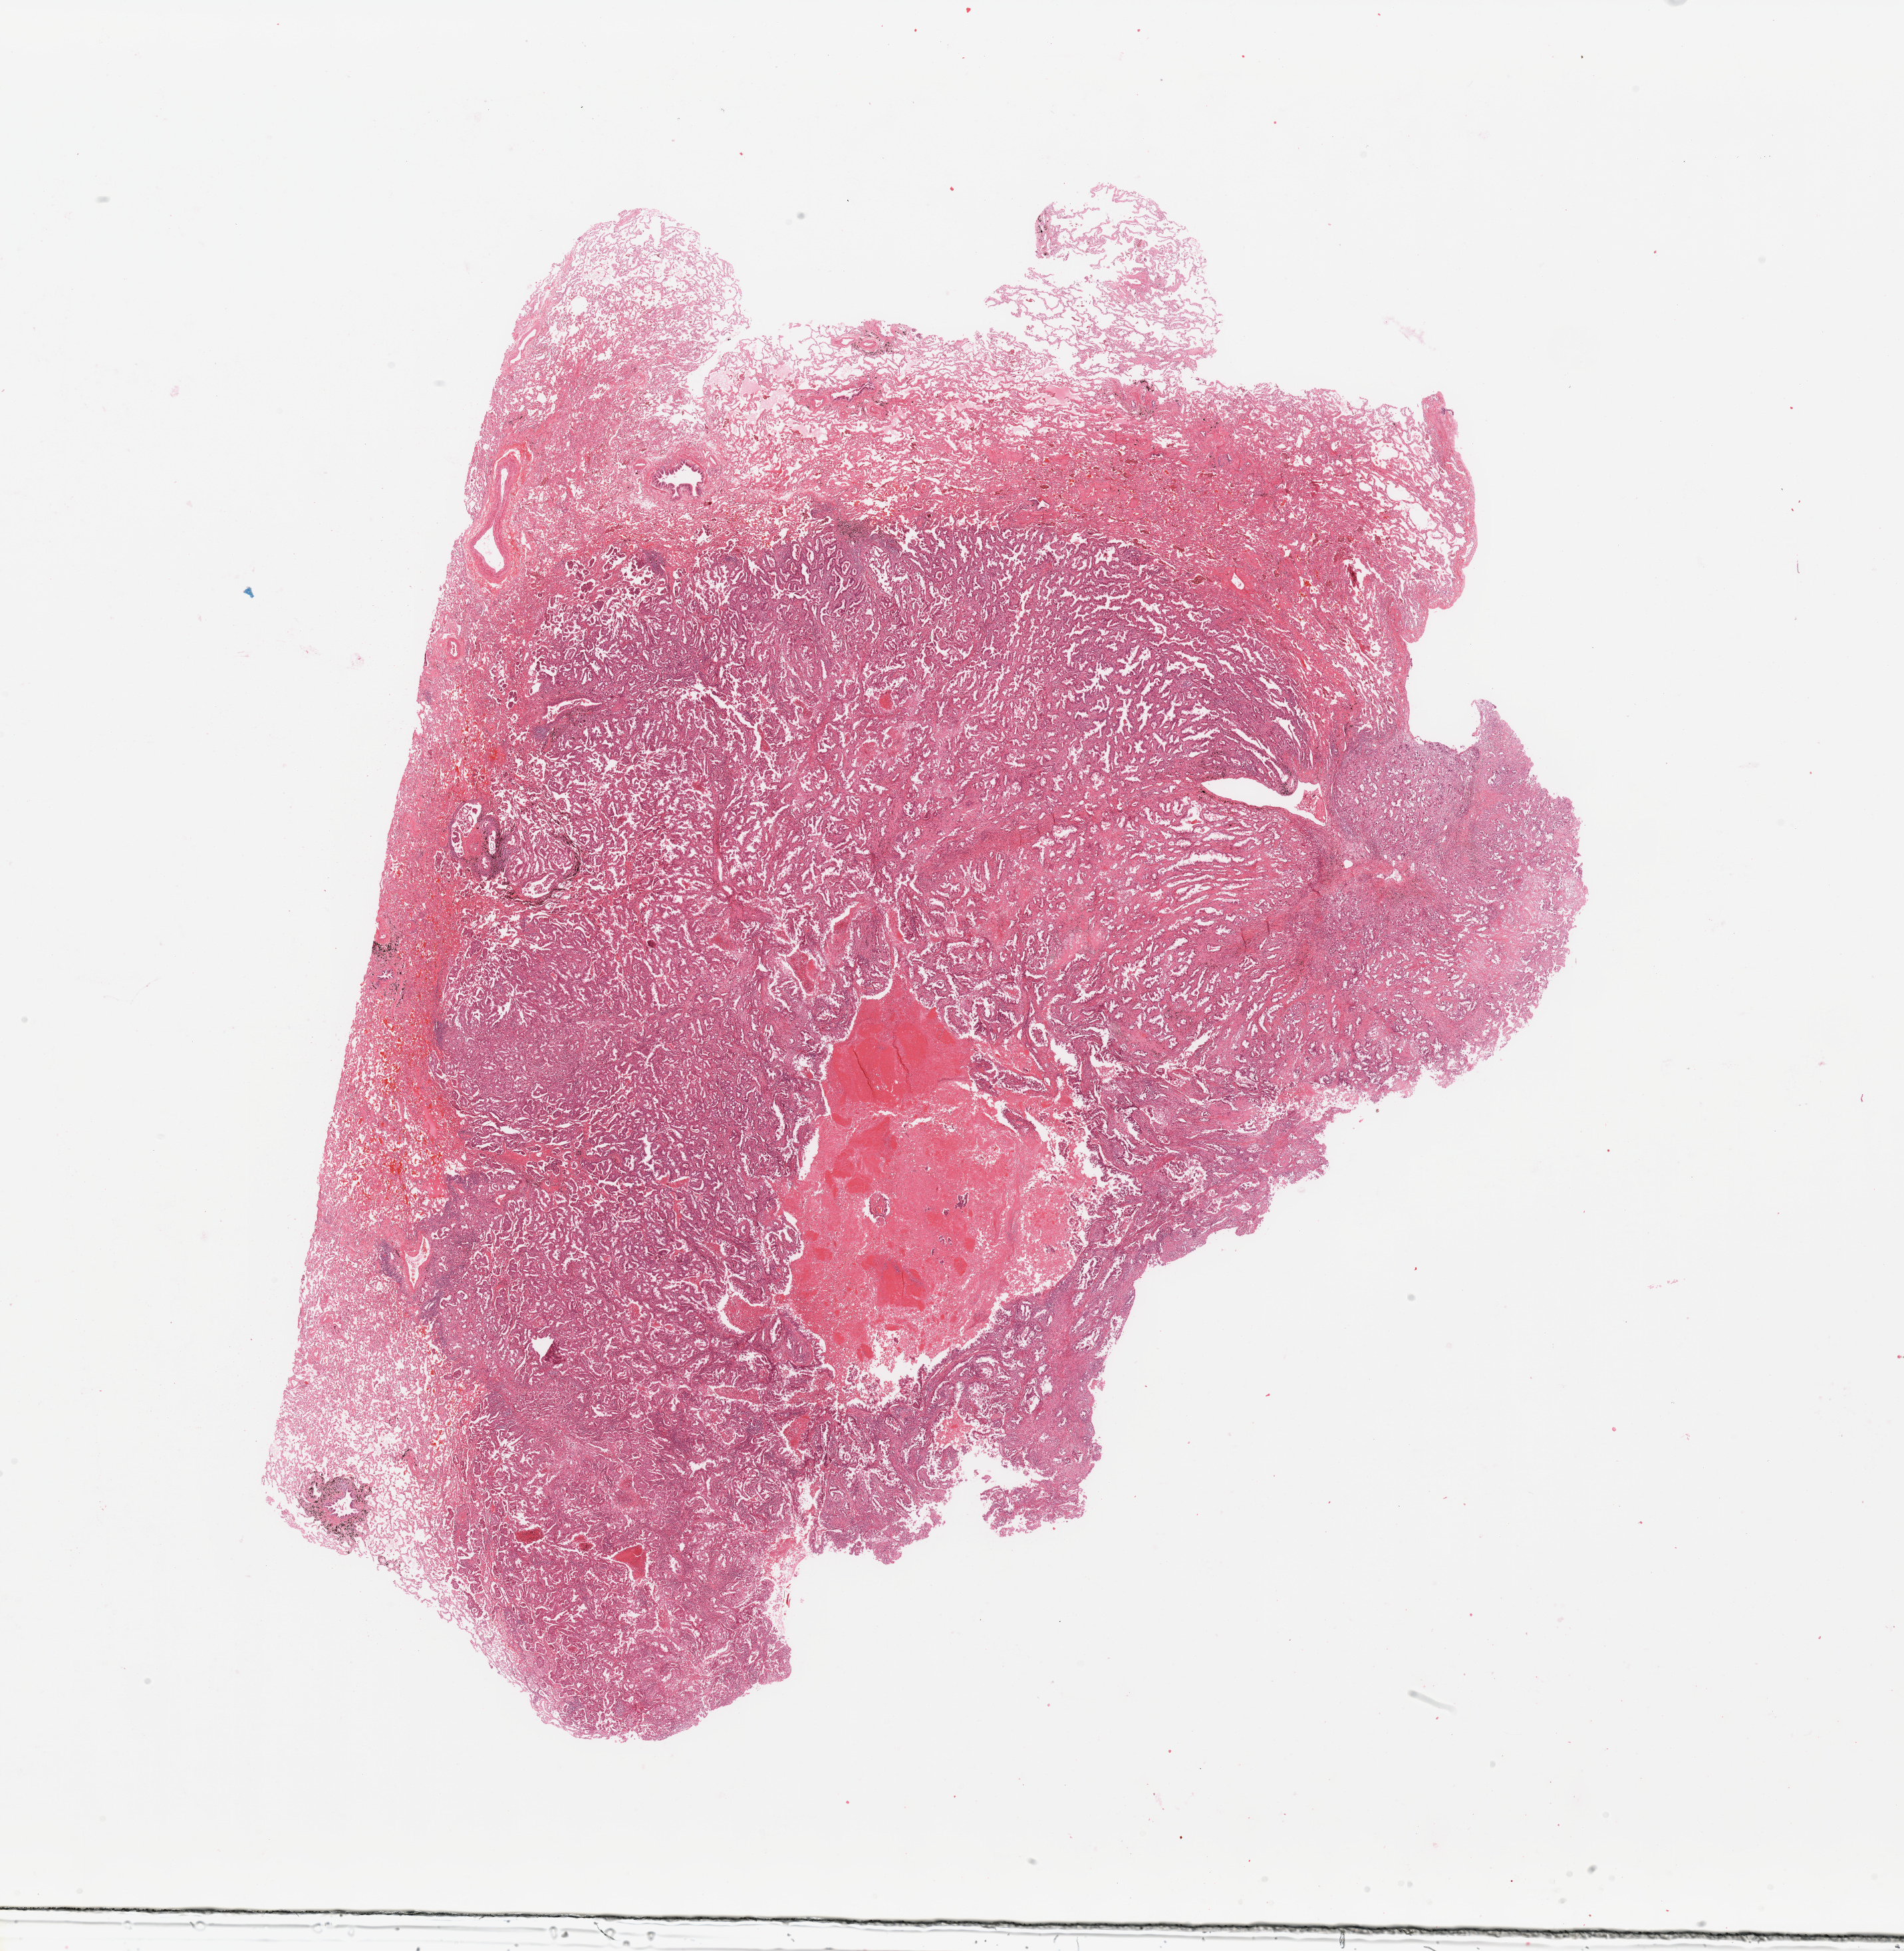
Digitized H&E-stained tissue section (whole slide) — low-resolution overview of the scanned area, about 22.6 x 23.2 mm (acquisition: 20x scan), tumour tissue sample, sampled site: lung. Female, 67 y/o. Histologic grade: G2 (moderately differentiated). Composition of this section per pathologist review: tumour nuclei 80%, necrosis 10%.
Diagnosis: Adenocarcinoma, NOS. AJCC pathologic stage: IIIA.